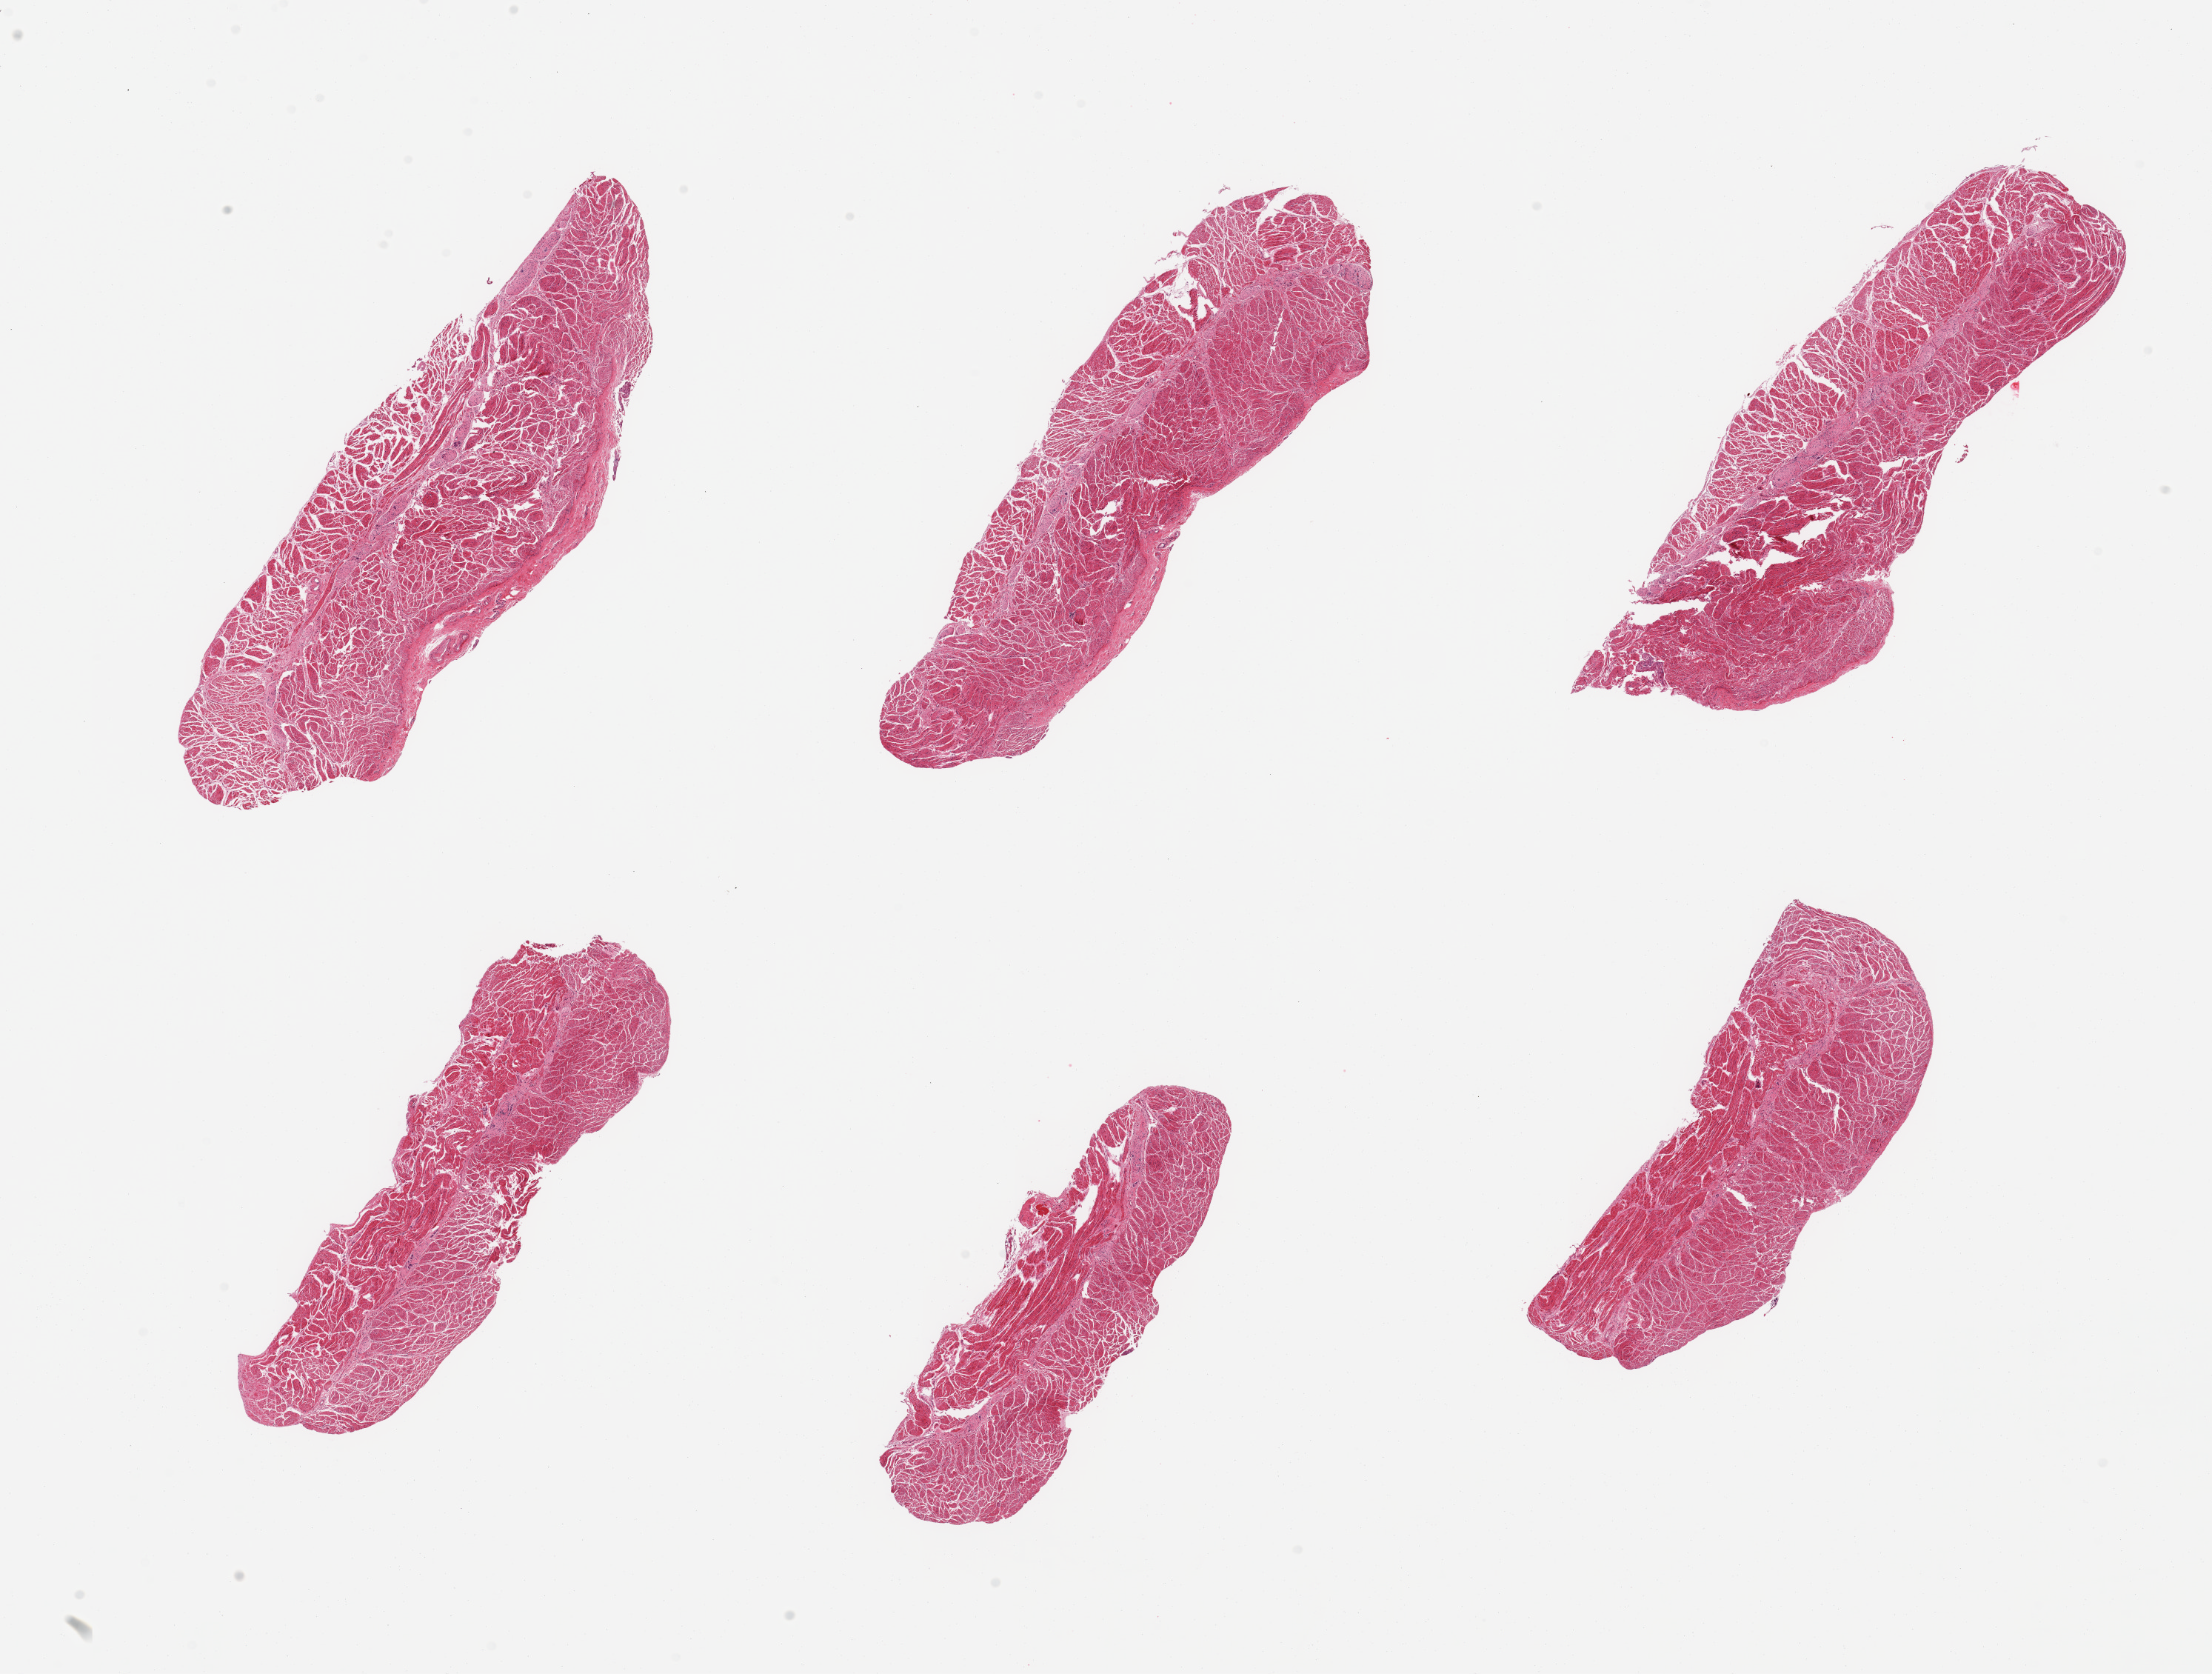
Whole-slide image, H&E stain, a low-resolution overview of the entire scanned area, about 23.6 x 17.9 mm, PAXgene-fixed, paraffin-embedded tissue, sampled site (target tissue): esophageal muscle, donor tissue sample.
Pathologist's review note for this sample: 6 pieces, confirmed target muscularis.